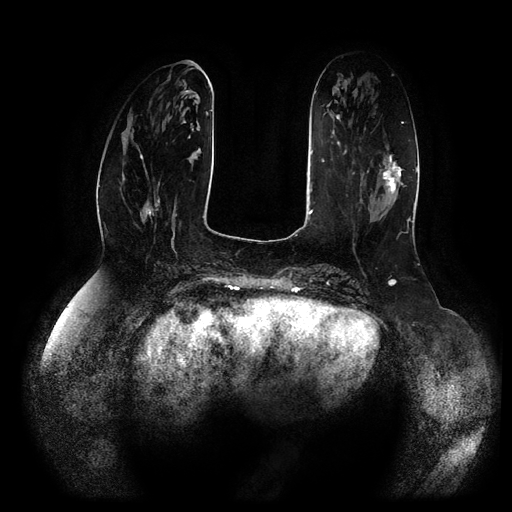
Breast MRI (dynamic contrast-enhanced, multi-phase), one axial slice; position 33 of 116 along the scan axis; dynamic contrast-enhanced series, time point 2 of 5 at this slice position (early post-contrast); 1.5 T; TE 2.5 ms, TR 5.2 ms; 2 mm slice thickness; 512 × 512 image matrix, field of view 400 × 400 mm. Female patient, age 66 years.
Annotated regions visible in this slice (semi-automatically segmented with operator editing):
- breast lesion (labelled 'tumour' in the annotation; benign lesions carry a separate 'benign' label): box from (x=379, y=149) to (x=406, y=201) px